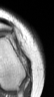
MRI of an extremity soft-tissue mass, one axial slice; position 13 of 42 along the scan axis; MR volume resampled by the dataset authors to the PET/CT grid (not the native acquisition matrix); 54 × 97 image matrix, field of view 53 × 95 mm. Female patient. From the clinical record (not read from this slice): histological type: spindle cell suggestive of biphasic synovial sarcoma; grade: intermediate; site of the primary tumour: left knee.
Outlined on this slice (expert contour drawn on MRI and transferred to this co-registered scan by the dataset authors):
- gross tumour volume including surrounding oedema: bounding box [x1, y1, x2, y2] px = [19, 53, 29, 67]